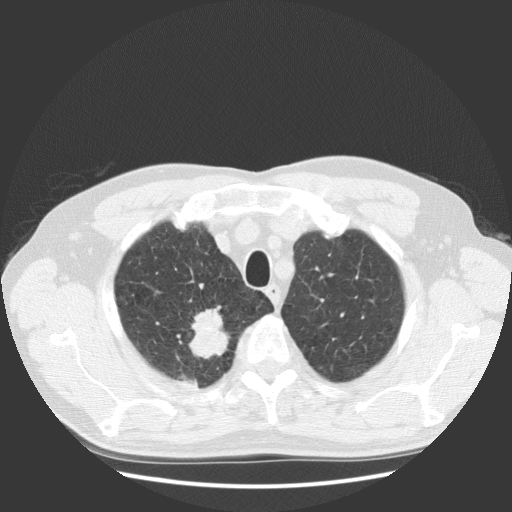
Axial slice from a low-dose chest CT screening exam, baseline screening round, lung window (W 1500 / L -600 HU), 2.5 mm slice thickness, standard (soft-tissue) reconstruction kernel (STANDARD), 512 × 512 image matrix, field of view 369 × 369 mm. Male participant, aged 63 years at enrolment. Current smoker at enrolment.
Lesion marked by an expert reader, bounding box <166,317,237,382> (left, top, right, bottom; pixels). The screening reader recorded 2 non-calcified nodules or masses ≥4 mm on this exam (right upper lobe, right upper lobe); which of them this box marks is not recorded. Official screen result: positive, change unspecified: nodule(s) >= 4 mm or enlarging nodule(s), mass(es), or other non-specific abnormalities suspicious for lung cancer. Participant outcome: lung cancer diagnosed 30 days after this screen — squamous cell carcinoma, NOS, right upper lobe, stage IIIB (AJCC 6th edition), 35 mm at pathology.